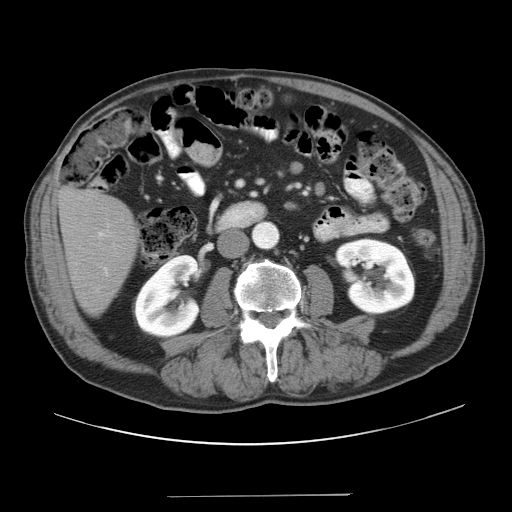
Contrast-enhanced abdominal CT, one axial slice. Slice 6 of 41 in the series (ordered by position). Reconstruction kernel STANDARD. 120 kVp. Intravenous contrast given. Soft-tissue window (W 400 / L 40 HU). 5 mm slice thickness. 512 × 512 image matrix. Male patient, age 75 years. Case-level facts recorded for this patient, not image findings: diagnosis: colorectal cancer liver metastases, imaged before liver resection; multiple liver metastases: no; largest metastasis: 5.2 cm; disease in both lobes: no.
Annotated regions visible in this slice (expert manual segmentation):
- liver: bounding box <60,190,136,313> (left, top, right, bottom; pixels)
- planned liver remnant (the part of the liver to remain after resection): <60,190,136,314>
- portal vein (with intrahepatic branches): <98,232,108,275>